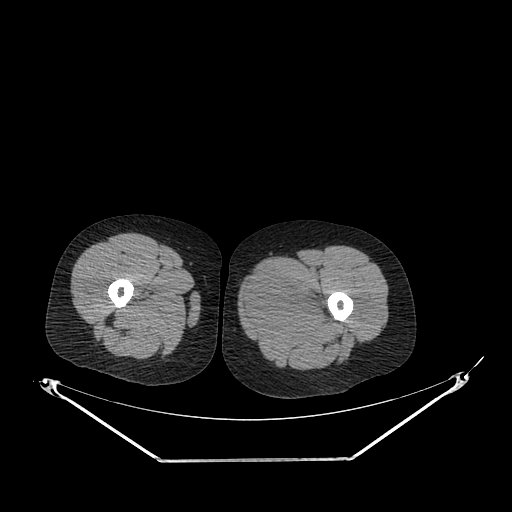
CT of an extremity soft-tissue mass (from a PET/CT study), one axial slice; slice 230 of 267 in the series (ordered by position); reconstruction kernel SOFT; 120 kVp; soft-tissue window (W 400 / L 40 HU); 3.75 mm slice thickness; 512 × 512 image matrix. Female patient. Case-level facts recorded for this patient, not image findings: histological type: pleiomorphic leiomyosarcoma; grade: intermediate; site of the primary tumour: left thigh.
Outlined on this slice (expert contour drawn on MRI and transferred to this co-registered scan by the dataset authors):
- gross tumour volume including surrounding oedema: bounding box <242,269,330,332> (left, top, right, bottom; pixels)
- gross tumour volume (mass): <244,269,323,330>